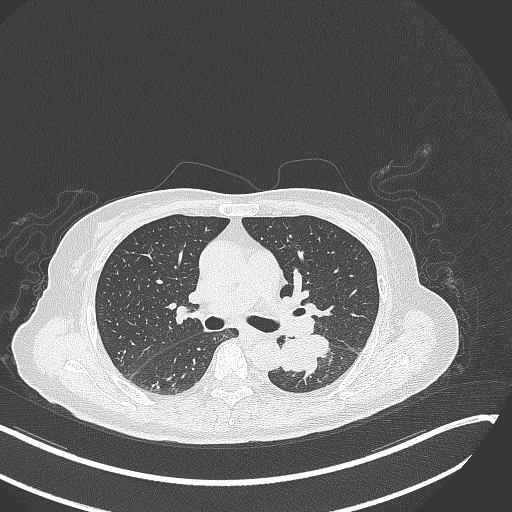
Chest CT, one axial slice; slice 169 of 342 in the series (ordered by position); reconstruction kernel B70f; 120 kVp; lung window (W 1500 / L -600 HU); 1 mm slice thickness; 512 × 512 image matrix, field of view 400 × 400 mm. Patient: female, 64 years. Case-level facts recorded for this patient, not image findings: clinical TNM (as recorded): T3 N1 M1; histopathological grade: G3.
Annotated regions visible in this slice (bounding box drawn by a radiologist):
- lung tumour (recorded histology: small cell carcinoma): bounding box [x1, y1, x2, y2] px = [279, 336, 330, 378]